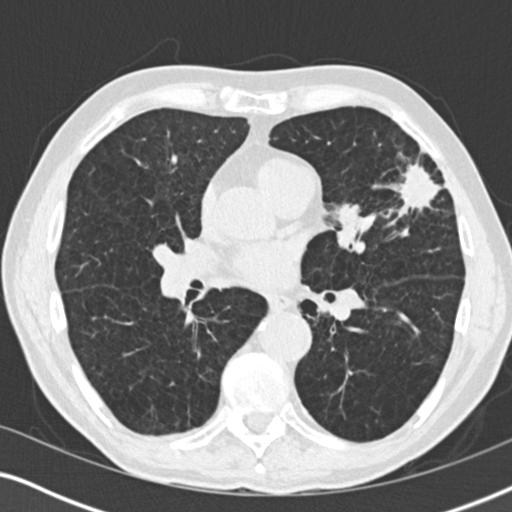
Low-dose screening chest CT, one axial slice; position 98 of 196 along the scan axis; reconstruction kernel B30f; 120 kVp; lung window (W 1500 / L -600 HU); 2 mm slice thickness; 512 × 512 image matrix.
Structures marked on this image (manually delineated by an expert):
- lesion 1 (tumor, upper lobe of left lung): box from (x=399, y=163) to (x=439, y=209) px
- lesion 2 (tumor, upper lobe of left lung): (x=339, y=204)–(x=360, y=226)